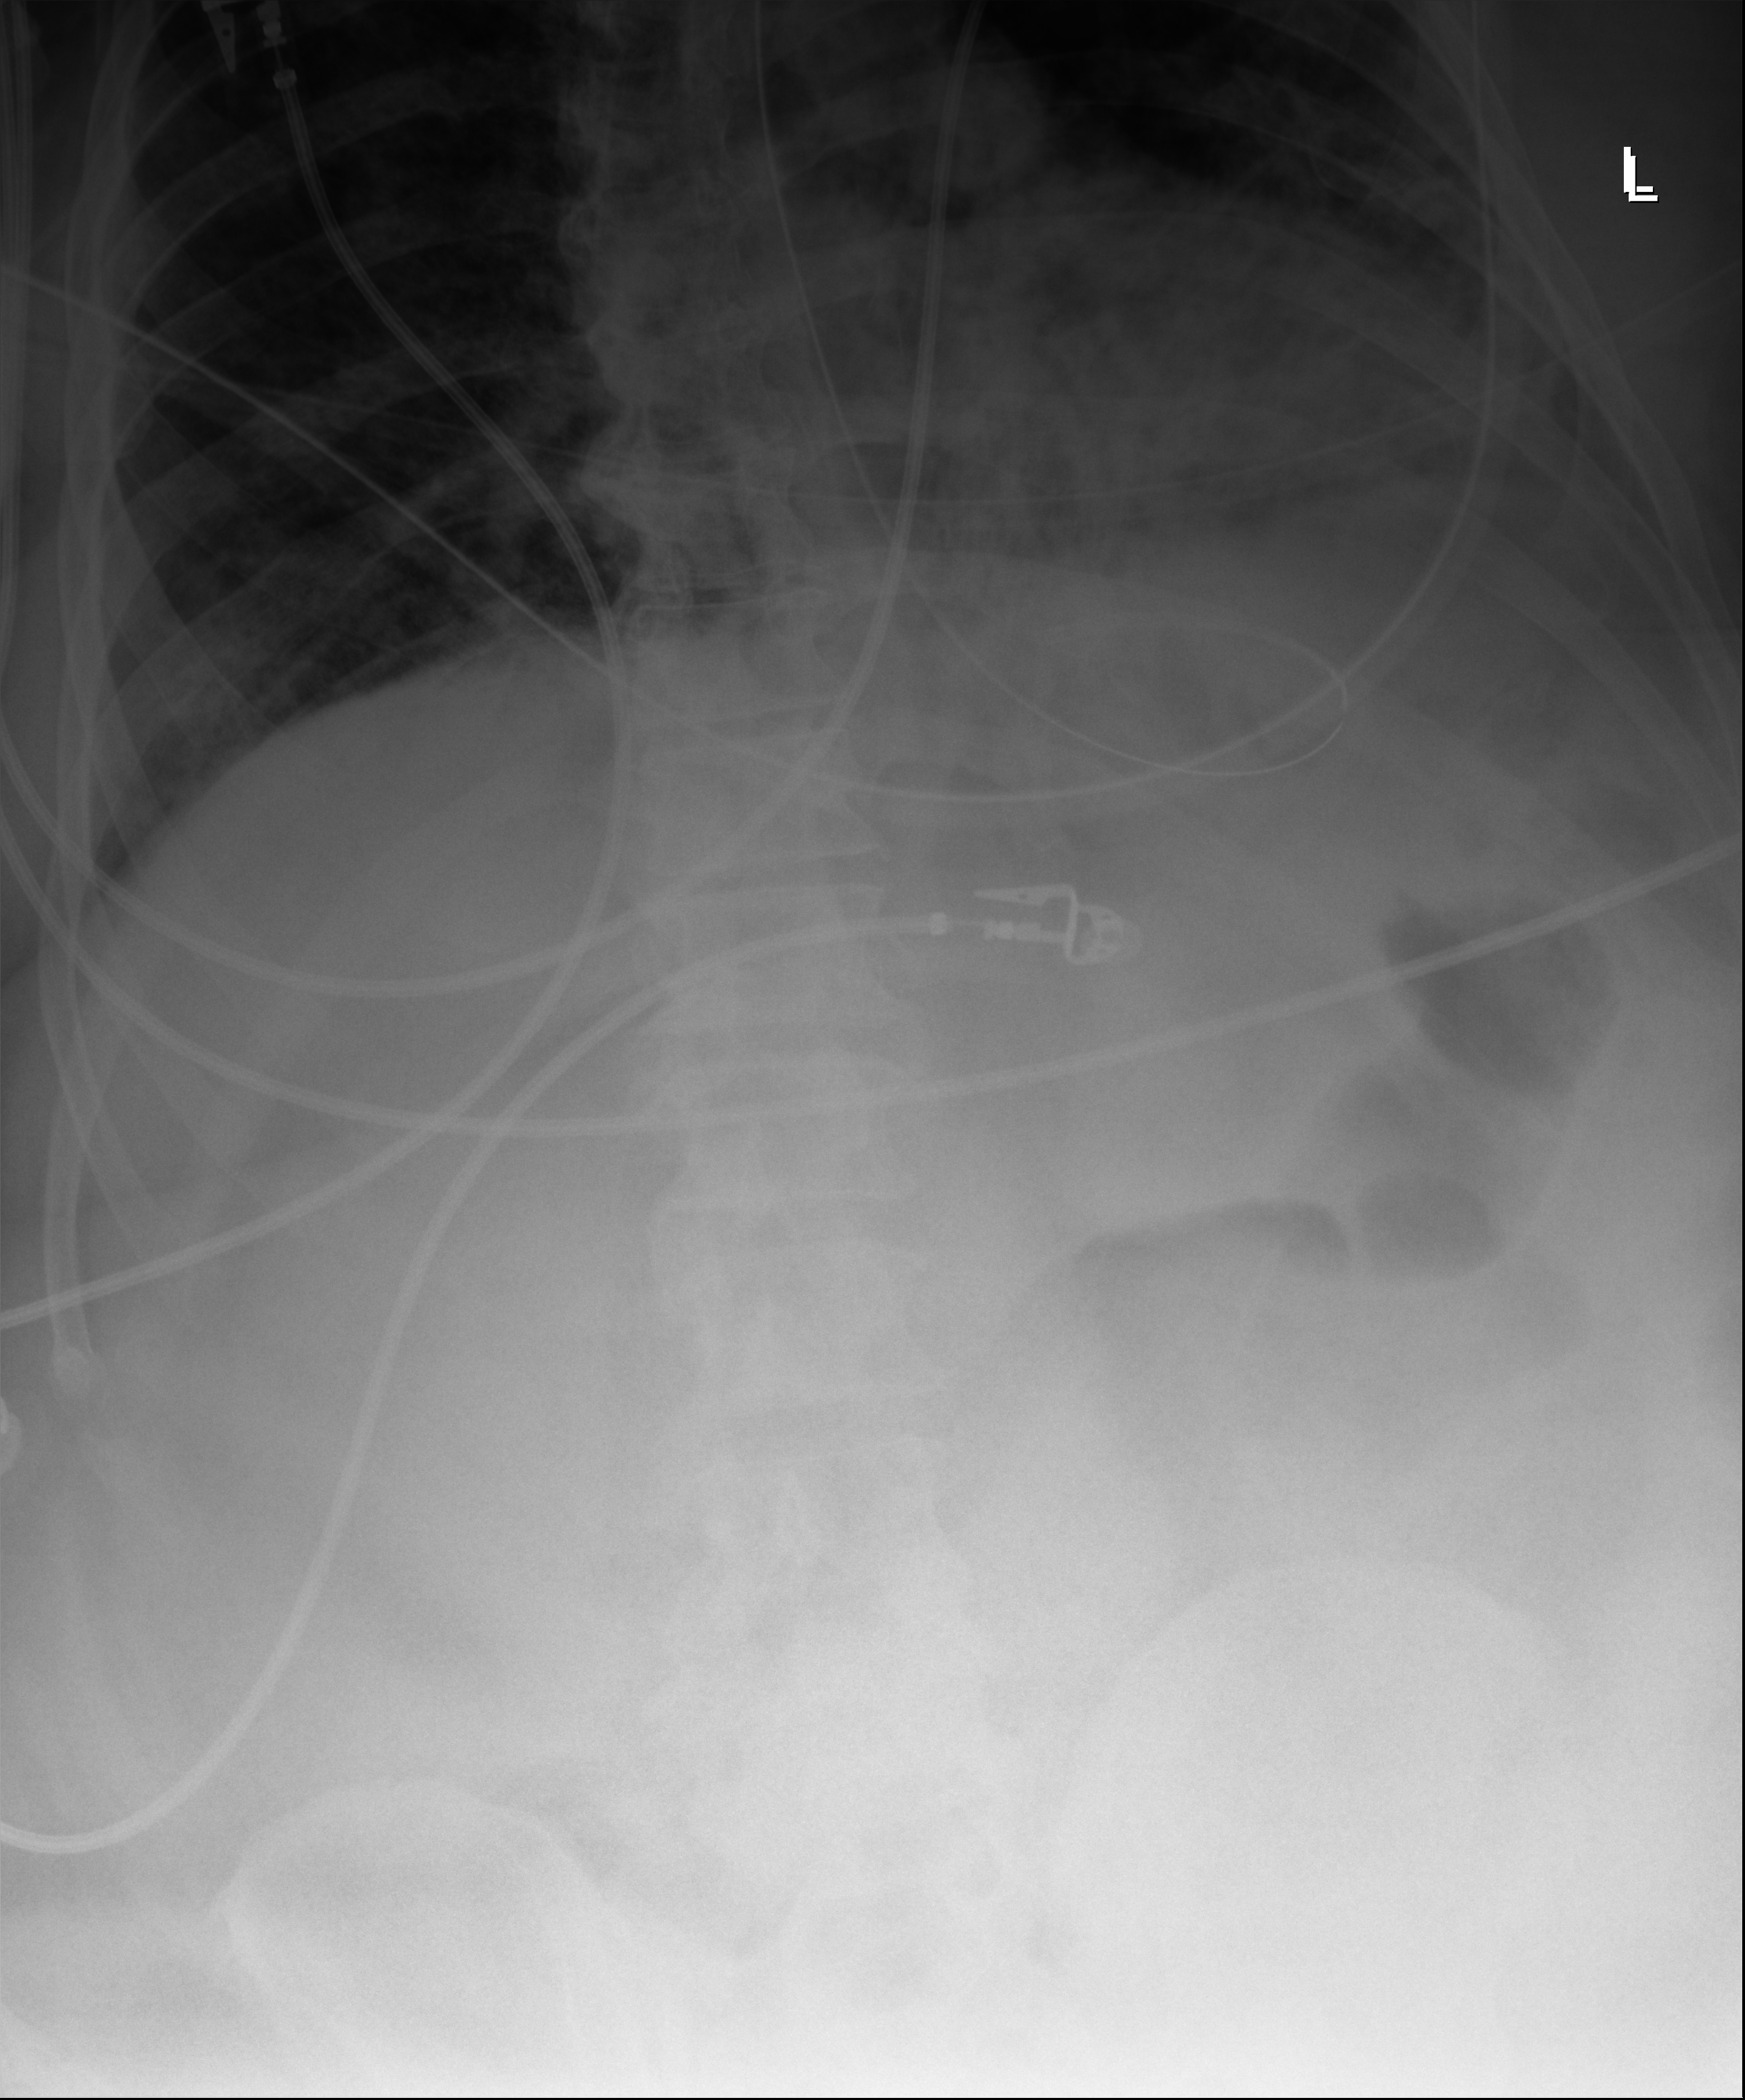
Portable abdomen radiograph. Adult patient hospitalised with COVID-19, age 18–59 years.
Admission-level facts for this patient (not findings on this image; timing relative to this image not recorded): mechanically ventilated during this hospital stay: yes.